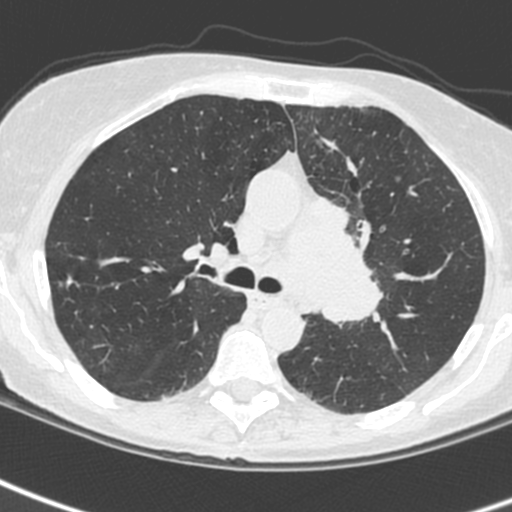
Low-dose screening chest CT, one axial slice. Position 160 of 242 along the scan axis. Lung window (W 1500 / L -600 HU). 1.3 mm slice thickness. 512 × 512 image matrix, field of view 284 × 284 mm.
Annotated regions visible in this slice (expert manual segmentation):
- lesion 3 (tumor, upper lobe of left lung): box from (x=307, y=195) to (x=383, y=324) px